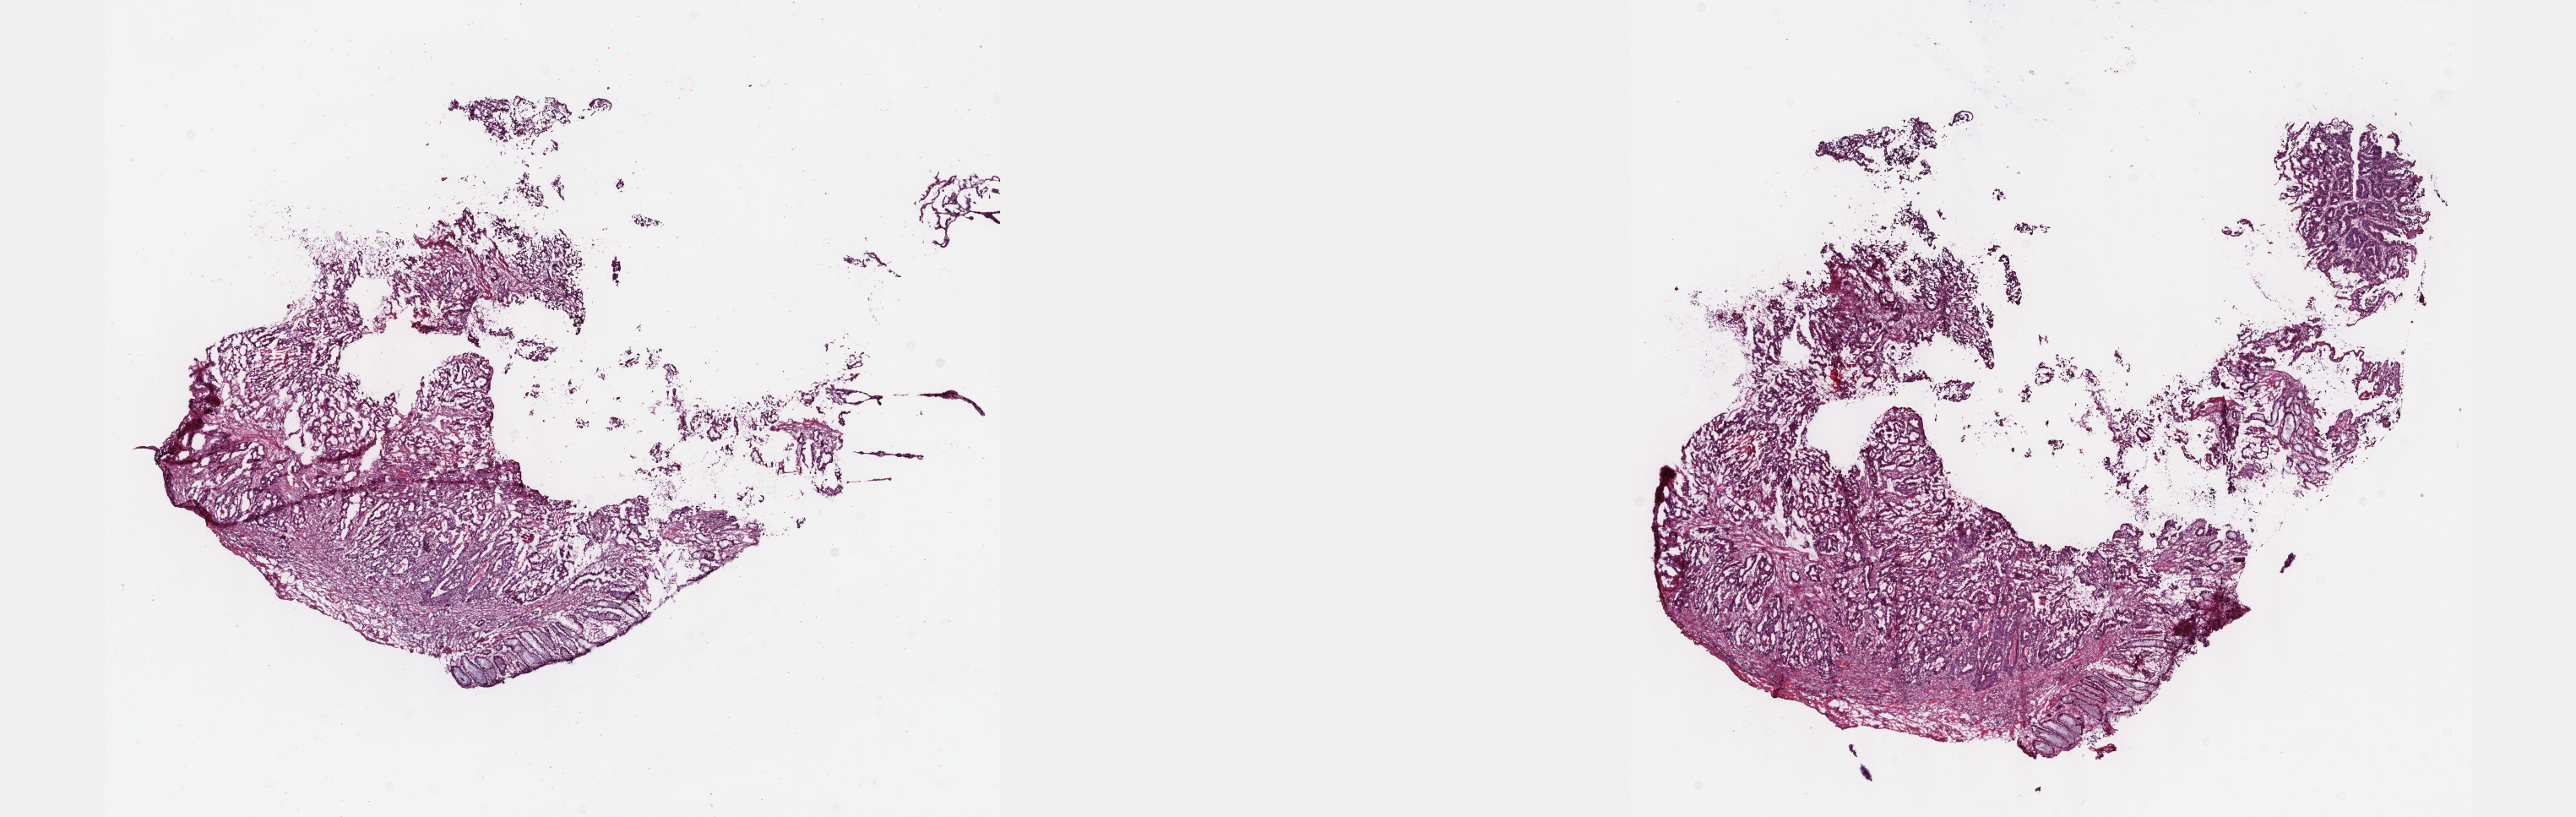
Hematoxylin and eosin (H&E) stained whole-slide image — a low-resolution overview of the entire scanned area, about 24.6 x 7.8 mm (acquisition: 40x scan); frozen section; colon, primary tumour sample. Female, age 74 years at initial diagnosis. Composition of this section per pathologist review: tumour cells 62%, tumour nuclei 70%, normal cells 20%, stromal cells 15%, necrosis 3%. Infiltration values recorded for this section: lymphocyte infiltration 16%, monocyte infiltration 3%, neutrophil infiltration 2%.
* AJCC pathologic stage: IV
* pathologic diagnosis: Adenocarcinoma, NOS (sigmoid colon)
* lymph nodes positive (case pathology): 6 of 12 examined